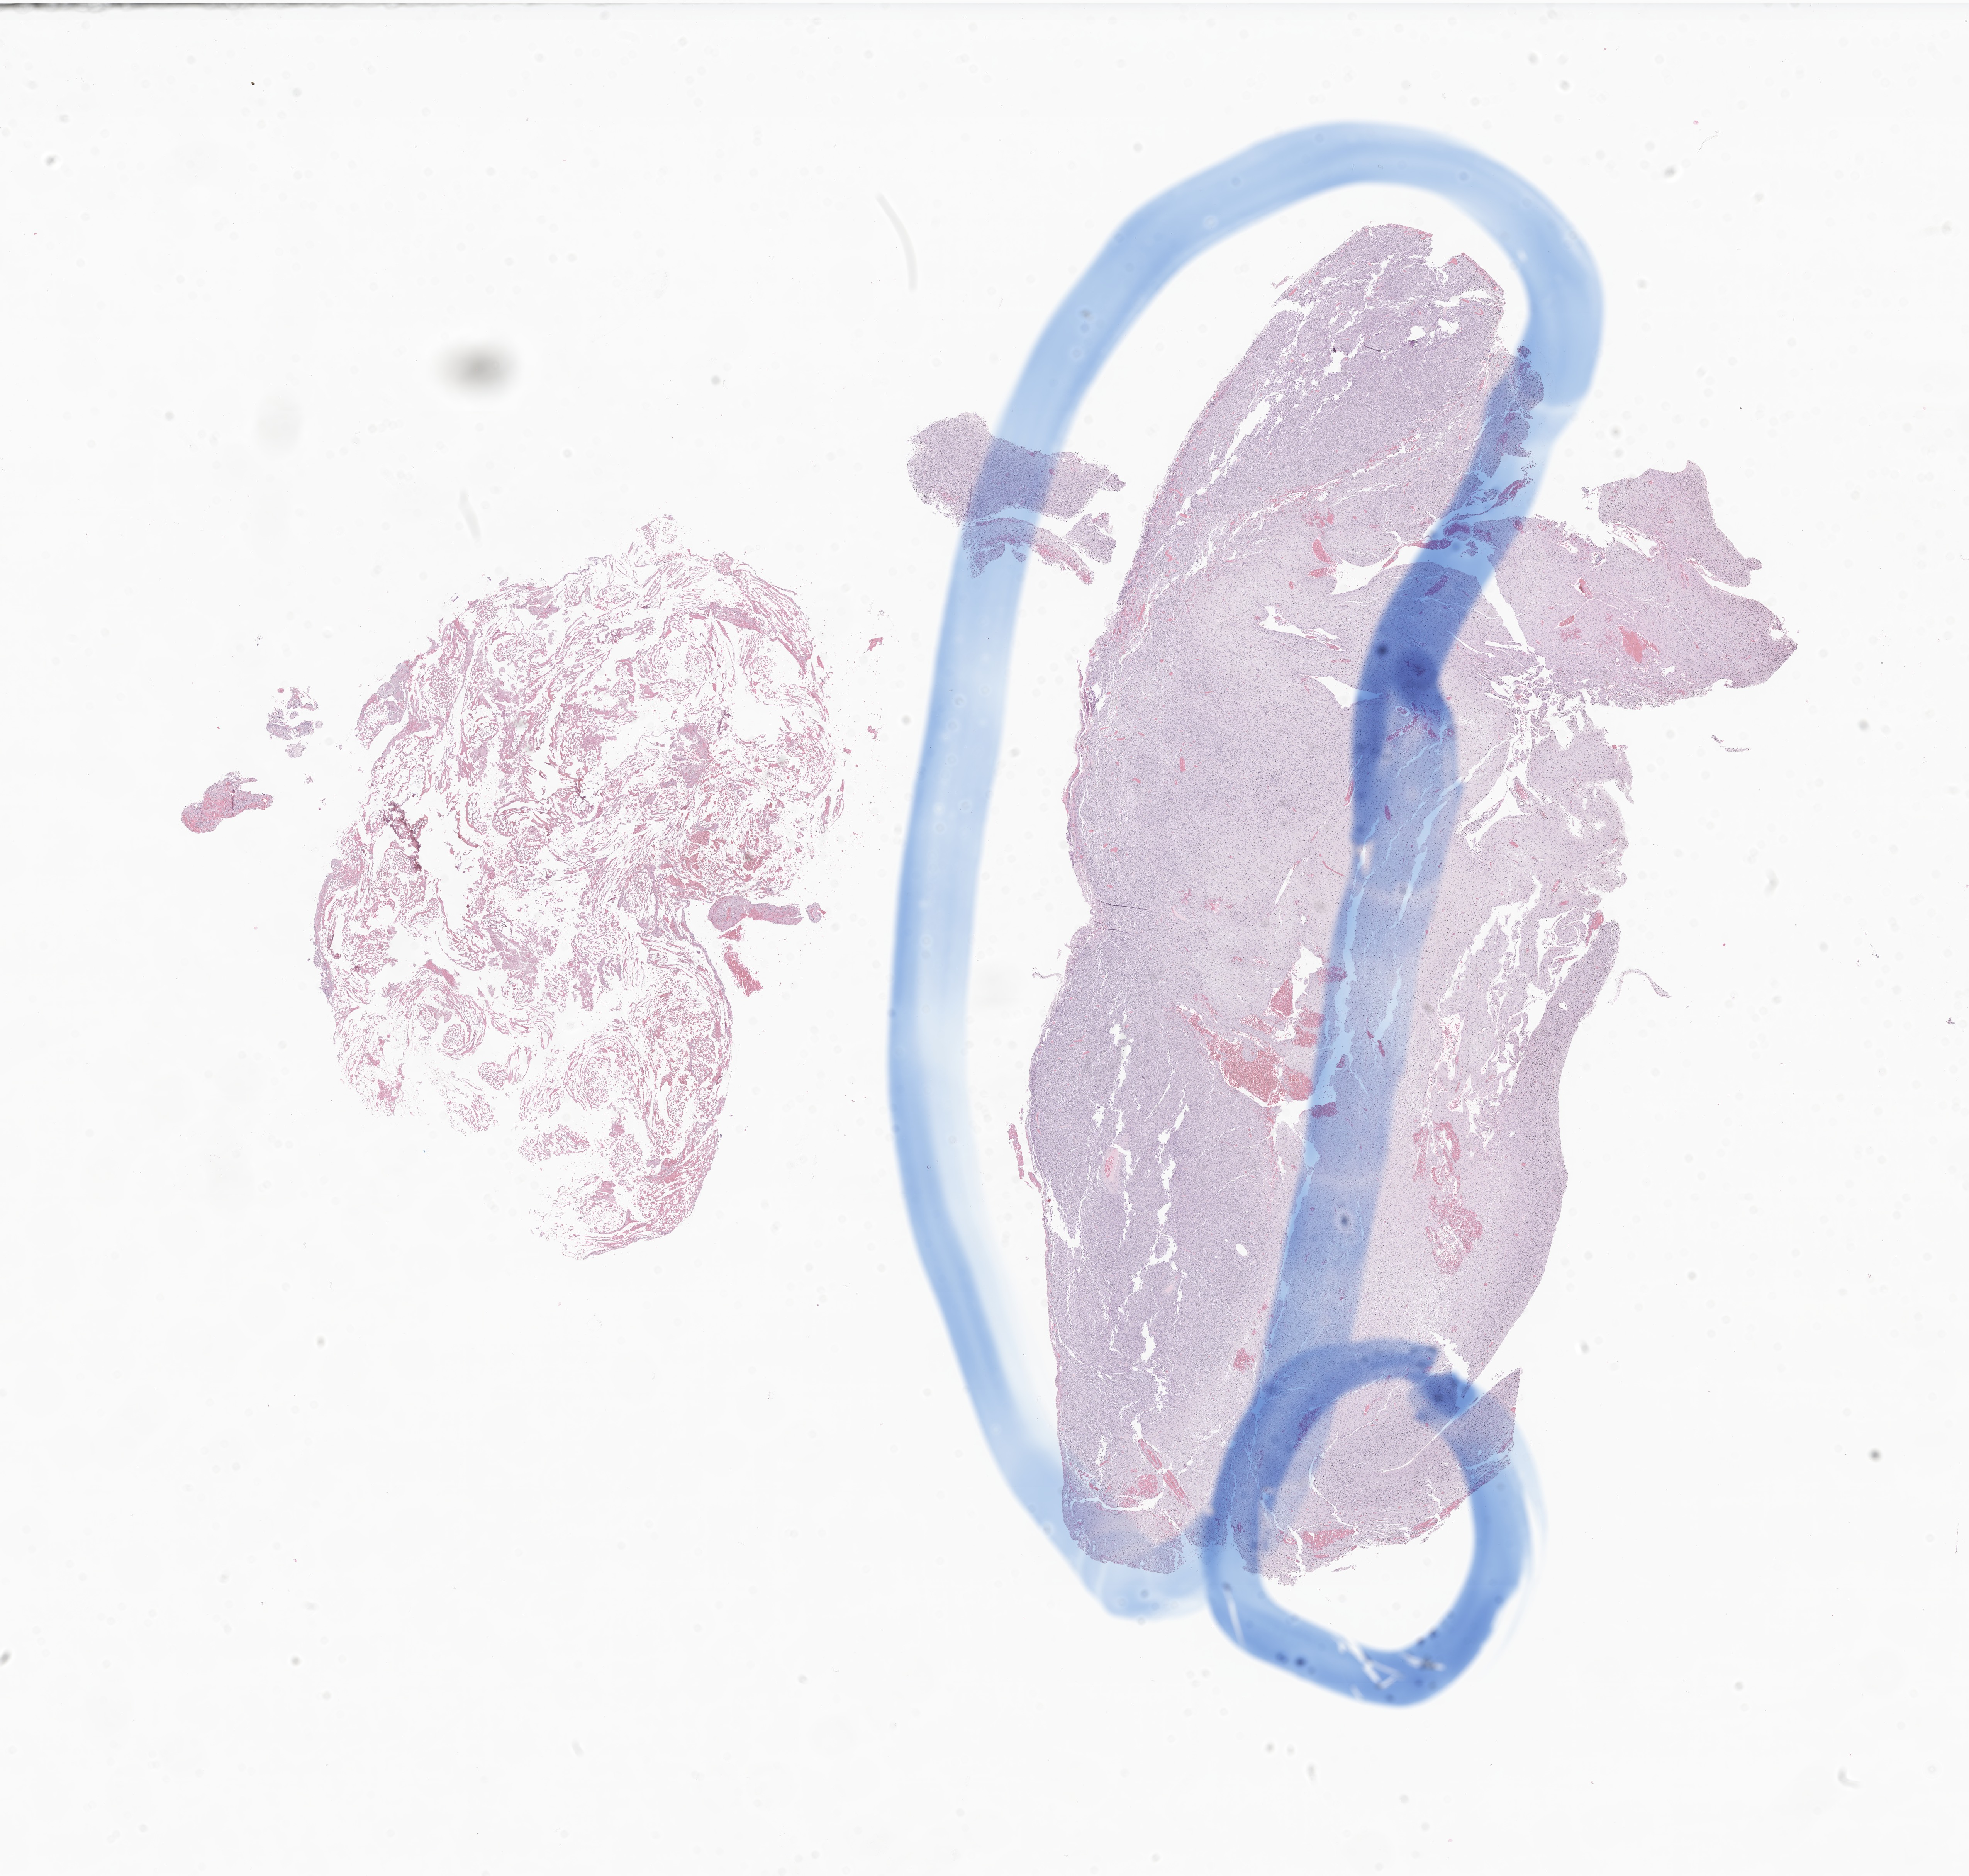
Digitized haematoxylin and eosin-stained section of tumor tissue from the brain — whole scanned area (about 21.5 x 20.5 mm) shown as a low-resolution overview; FFPE section. Male patient, age 163 months.
Recorded diagnosis: Pleomorphic xanthoastrocytoma, NOS.